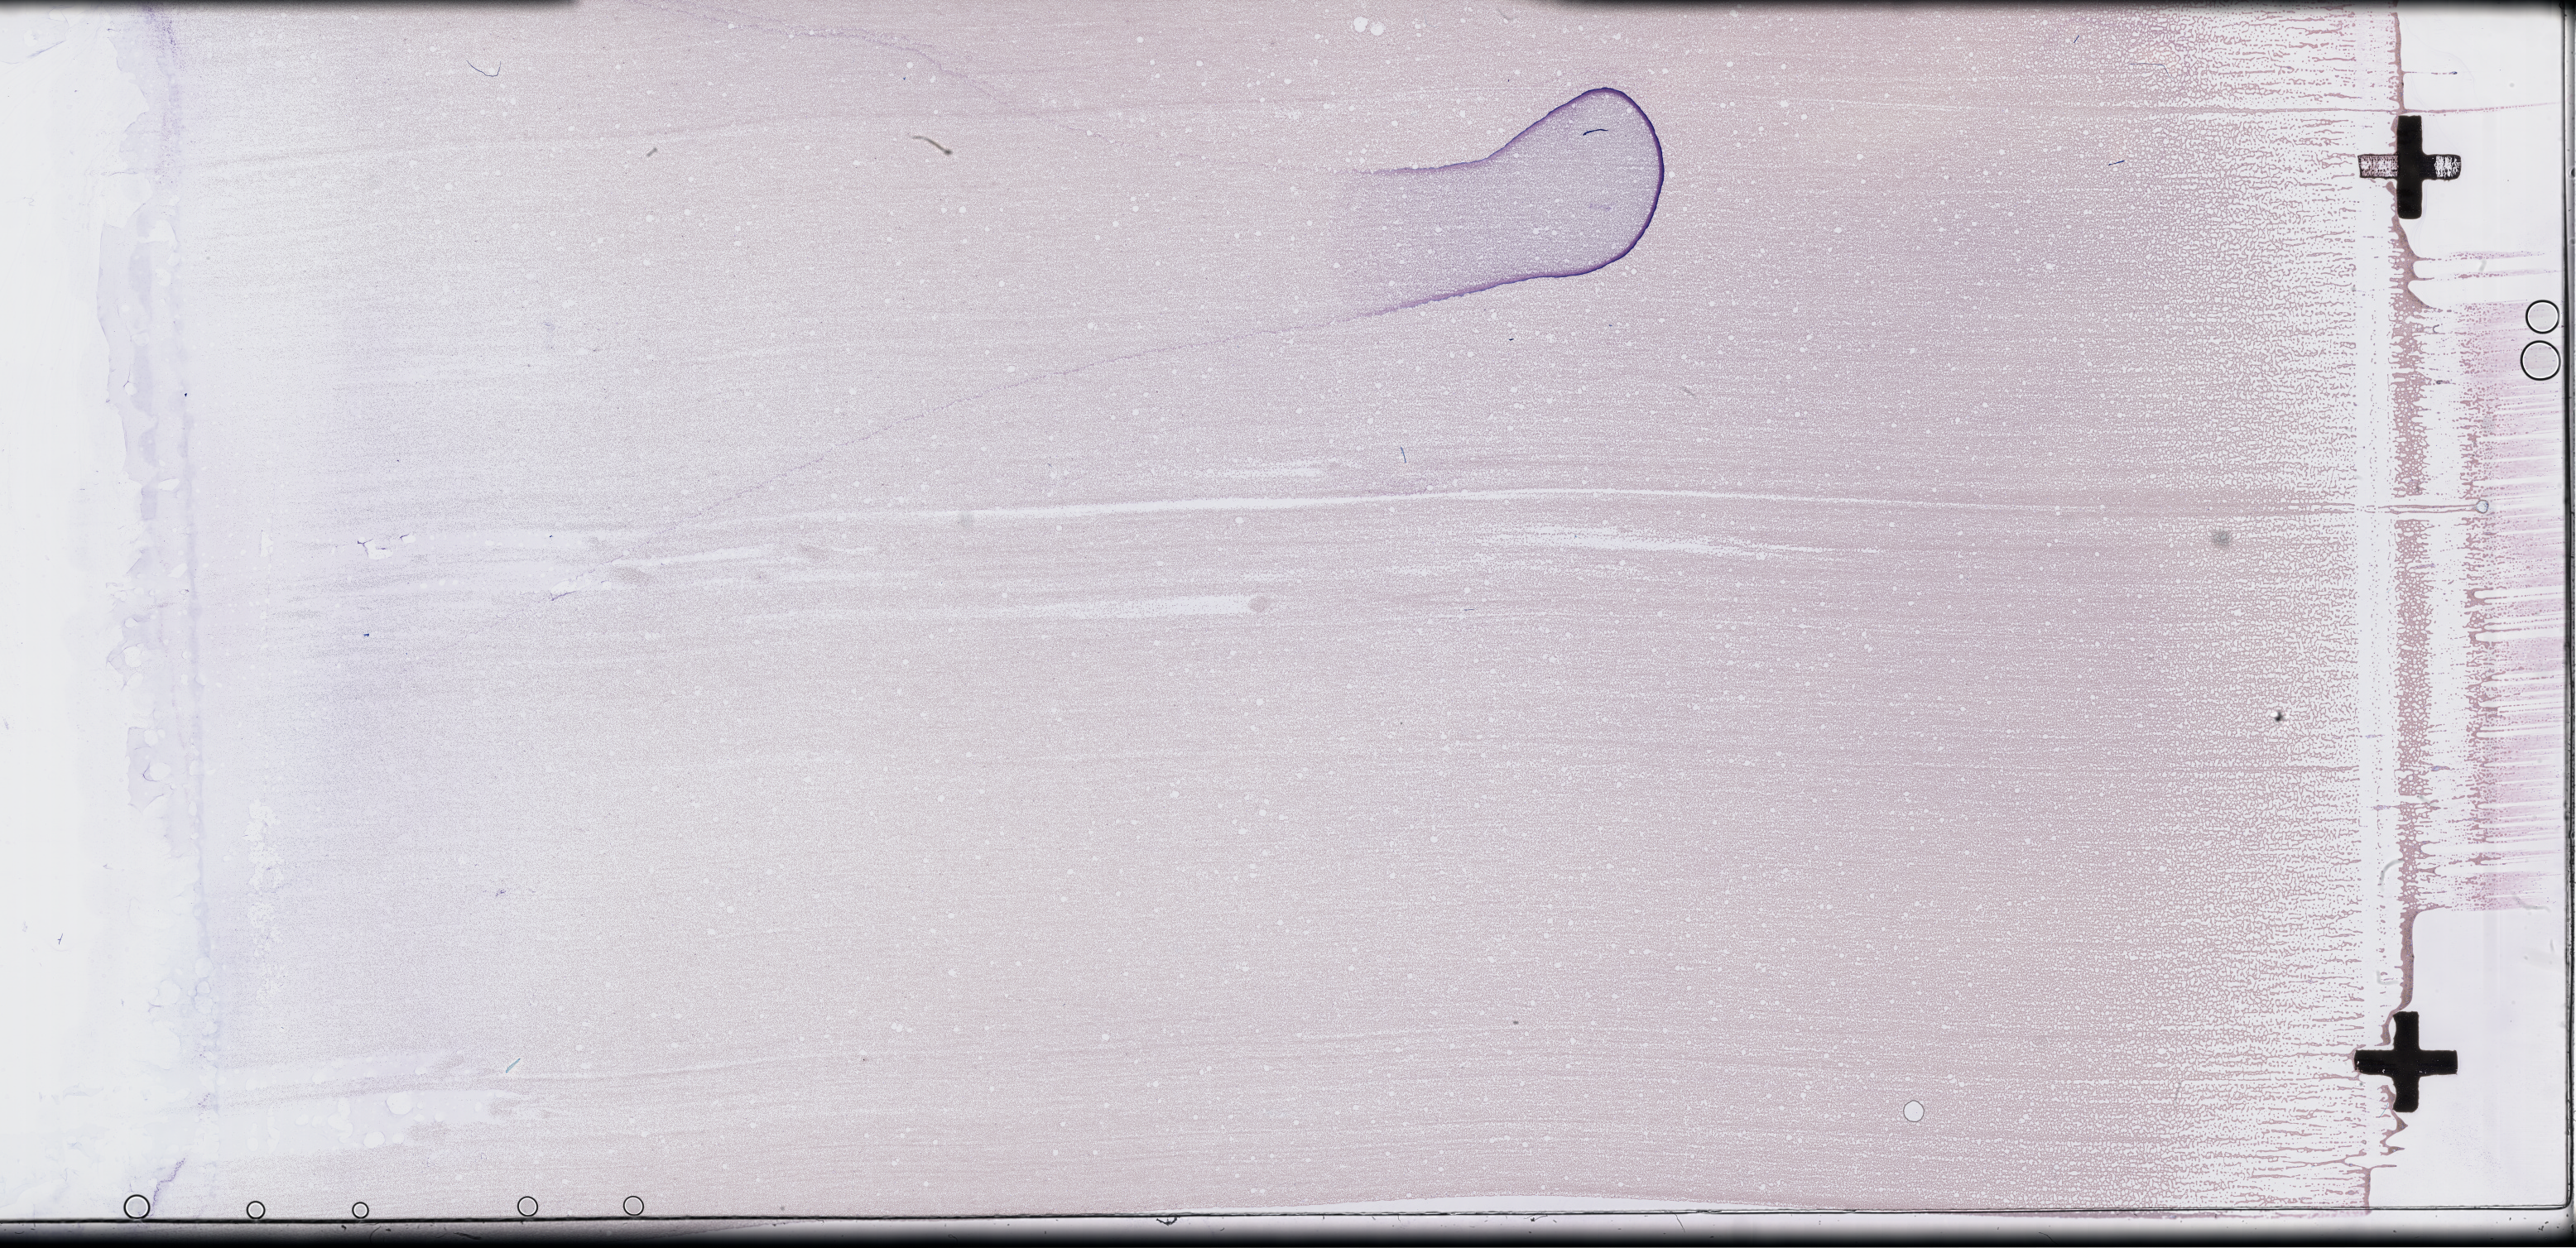
Whole-slide image of a whole blood smear, Wright-Giemsa stain, a low-resolution overview of the entire scanned area, about 50.3 x 24.4 mm; specimen time point: collected on treatment. Patient sex: male.
From a patient with: Plasma Cell Myeloma.